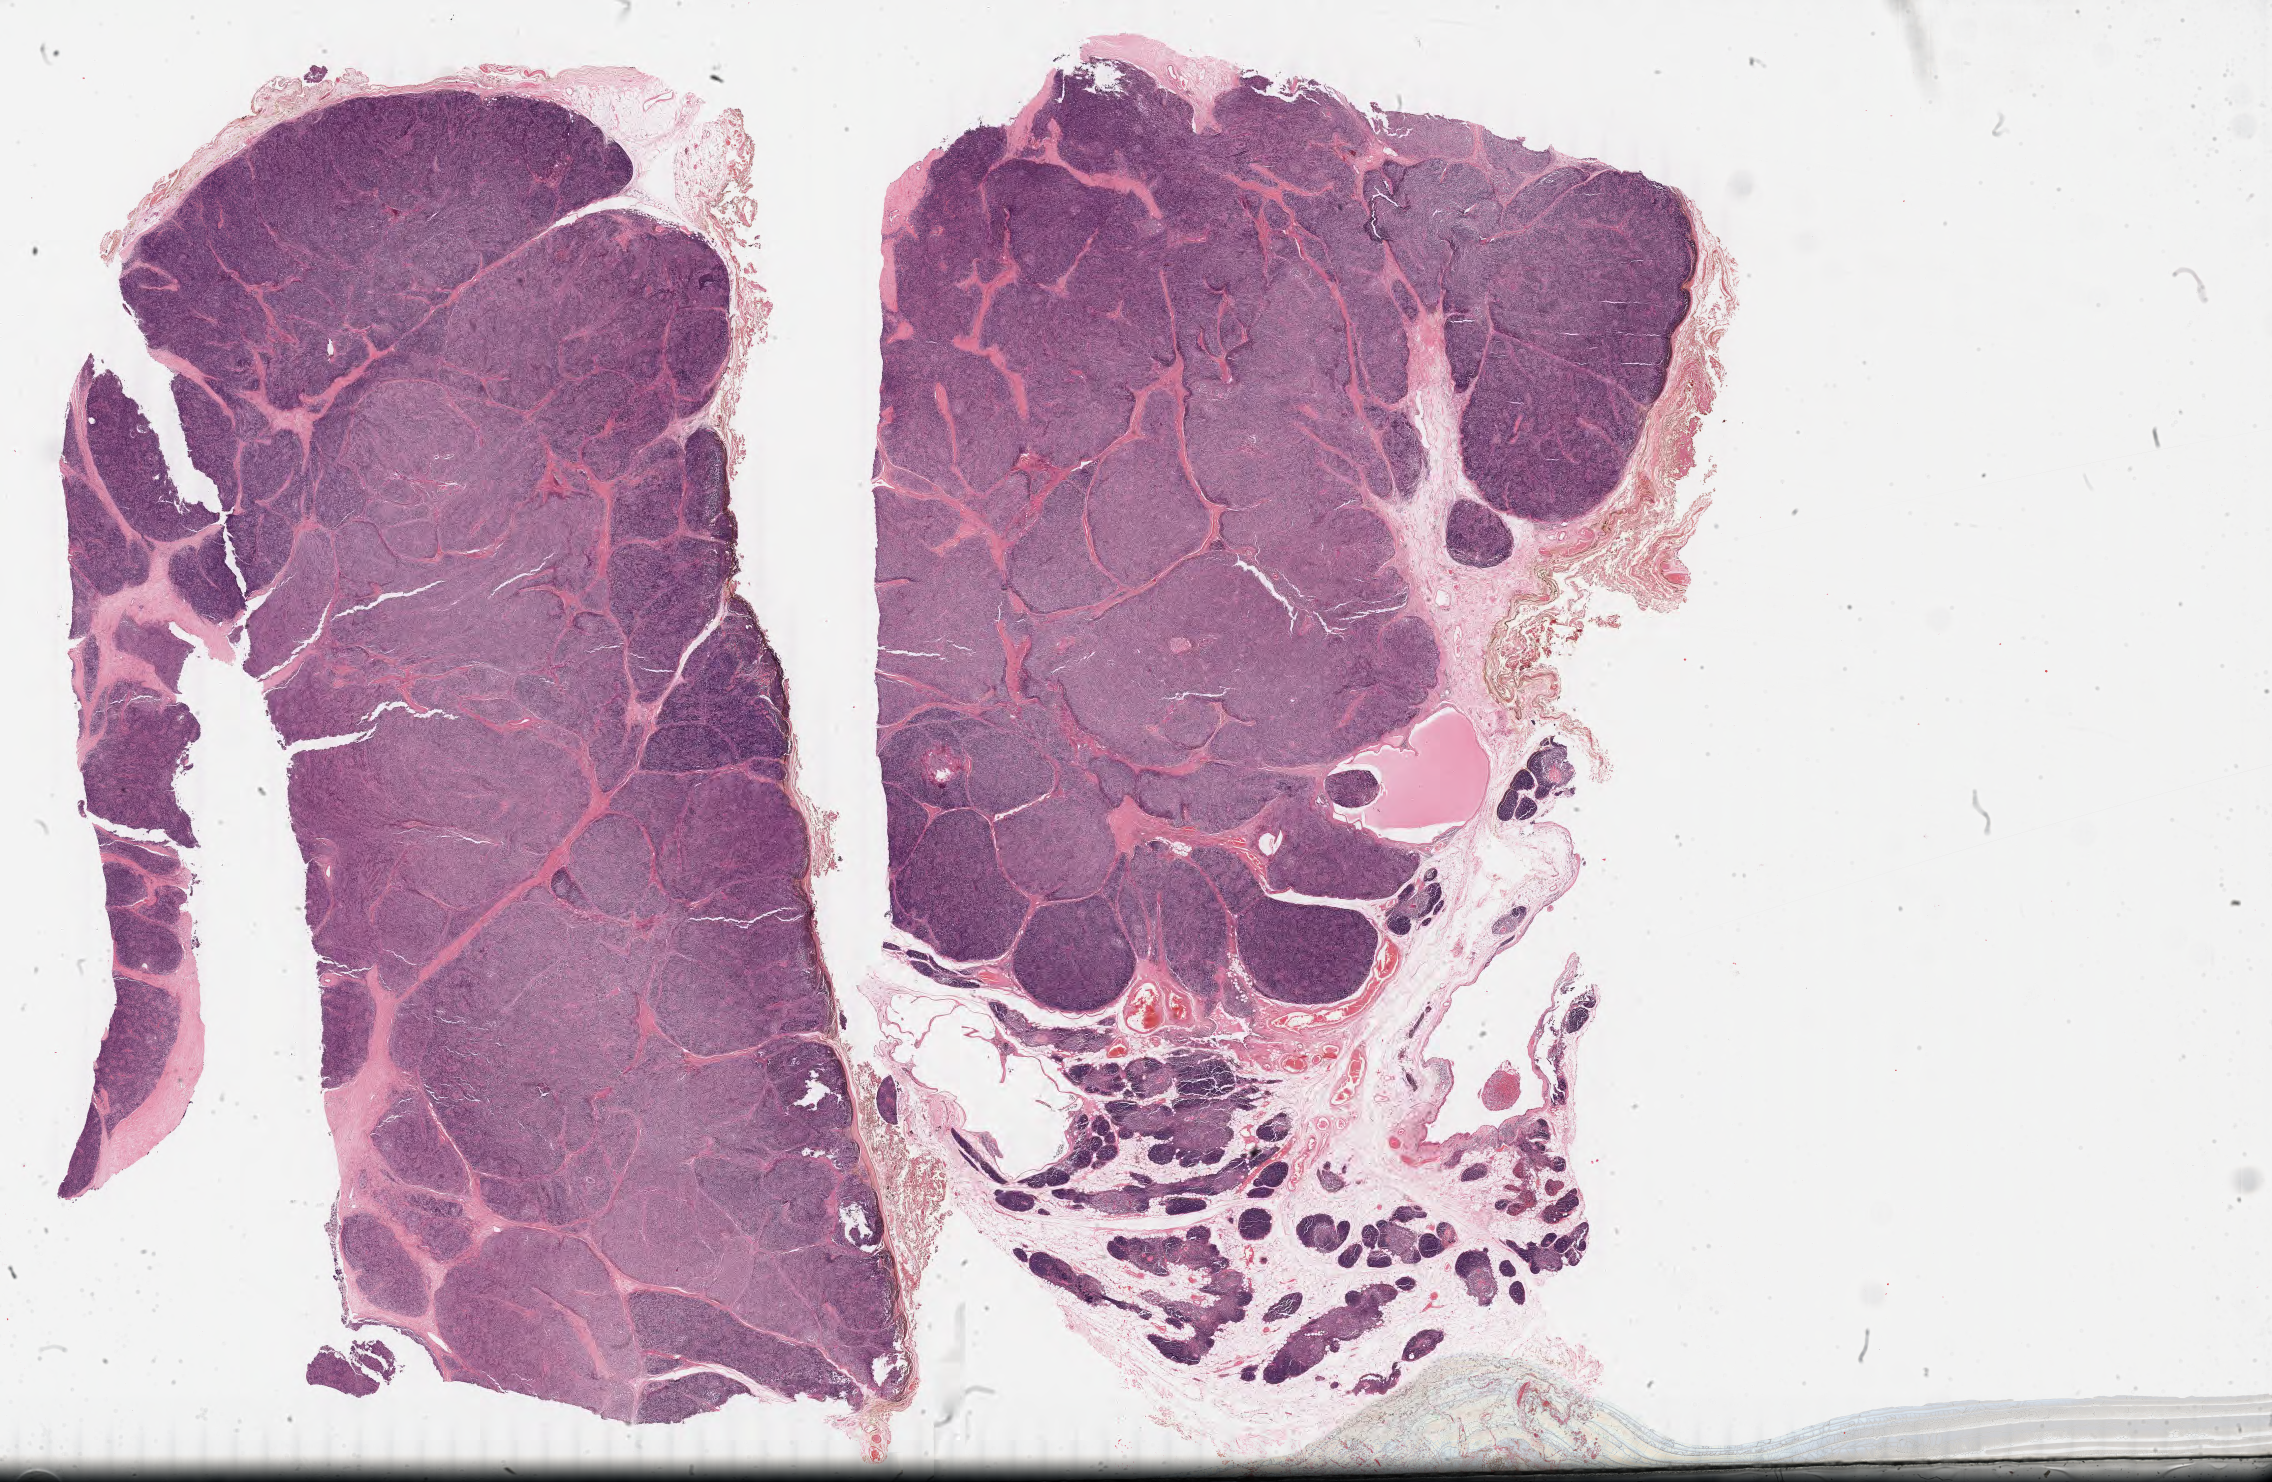
Digitized Hematoxylin and eosin (H&E) stained tissue section (whole slide), whole scanned area (about 35.9 x 23.4 mm, acquisition: 40x scan) shown as a low-resolution overview; formalin-fixed paraffin-embedded (FFPE) diagnostic section; sample: primary tumour, thymus. Female patient; age at initial diagnosis 45 years.
- pathologic diagnosis: Thymoma, type B2, malignant